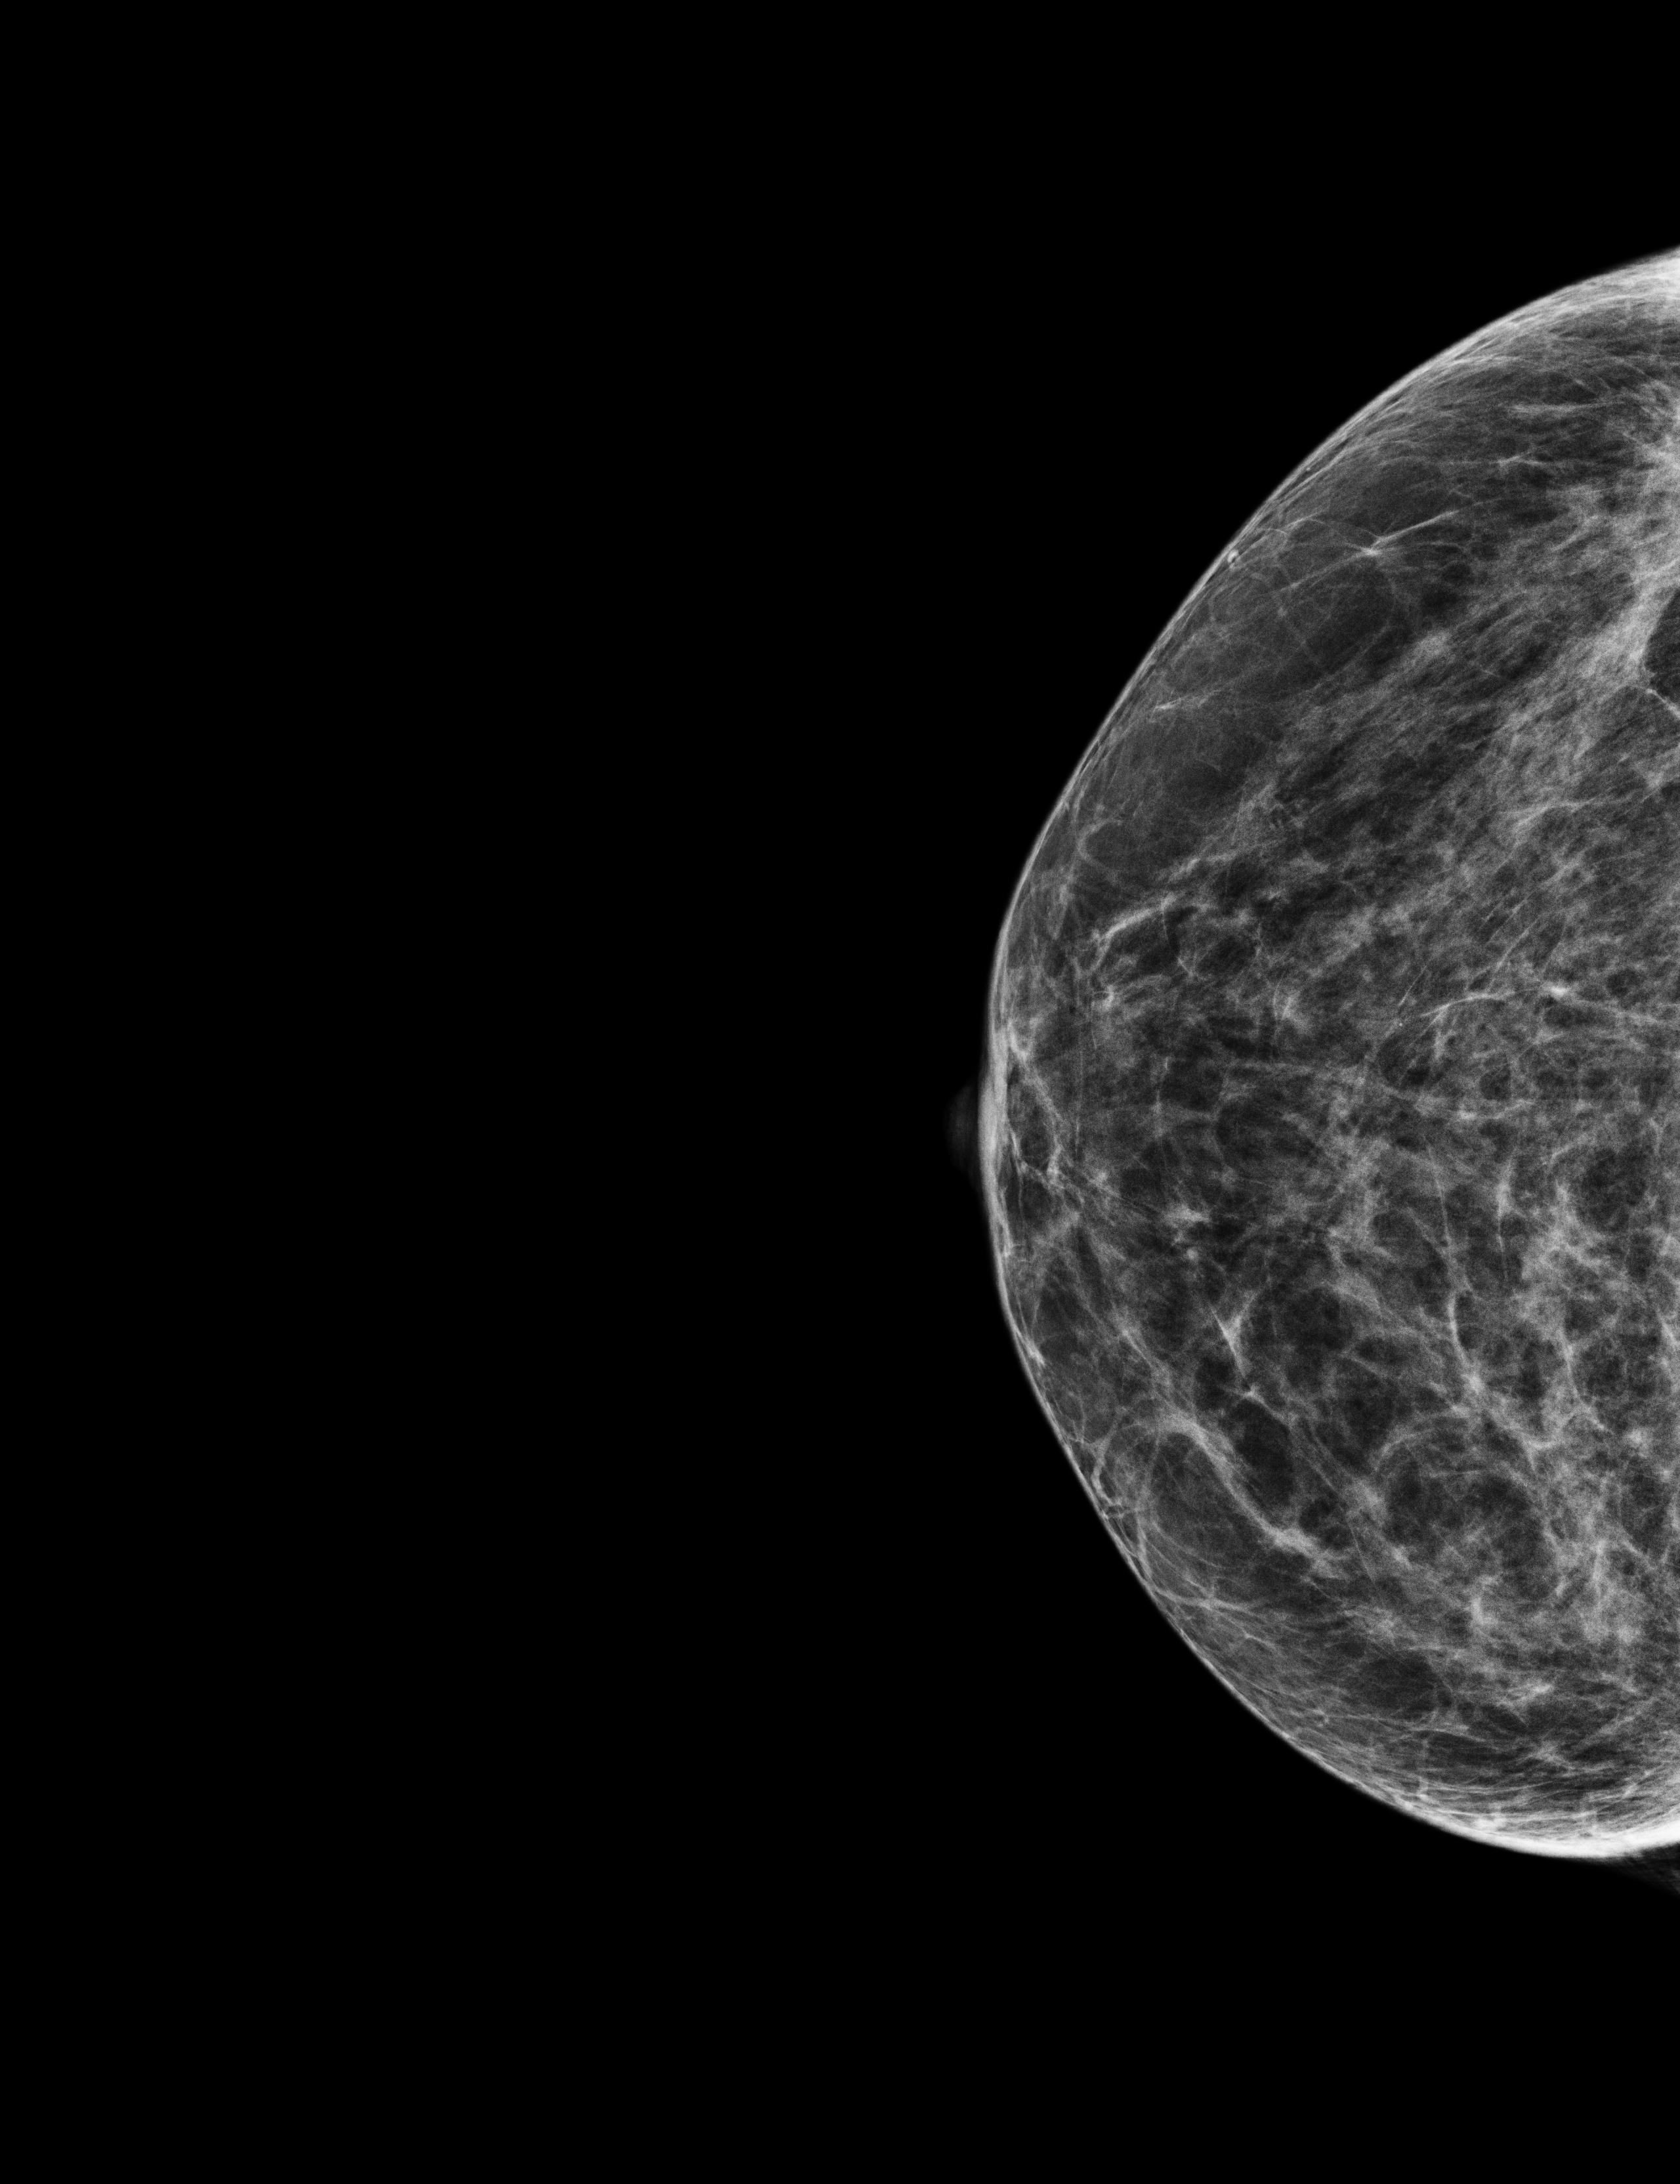
Annual screening mammography examination. Patient aged 65 years (female).
Image type: full-field digital mammogram. Breast: right. Projection: CC view.